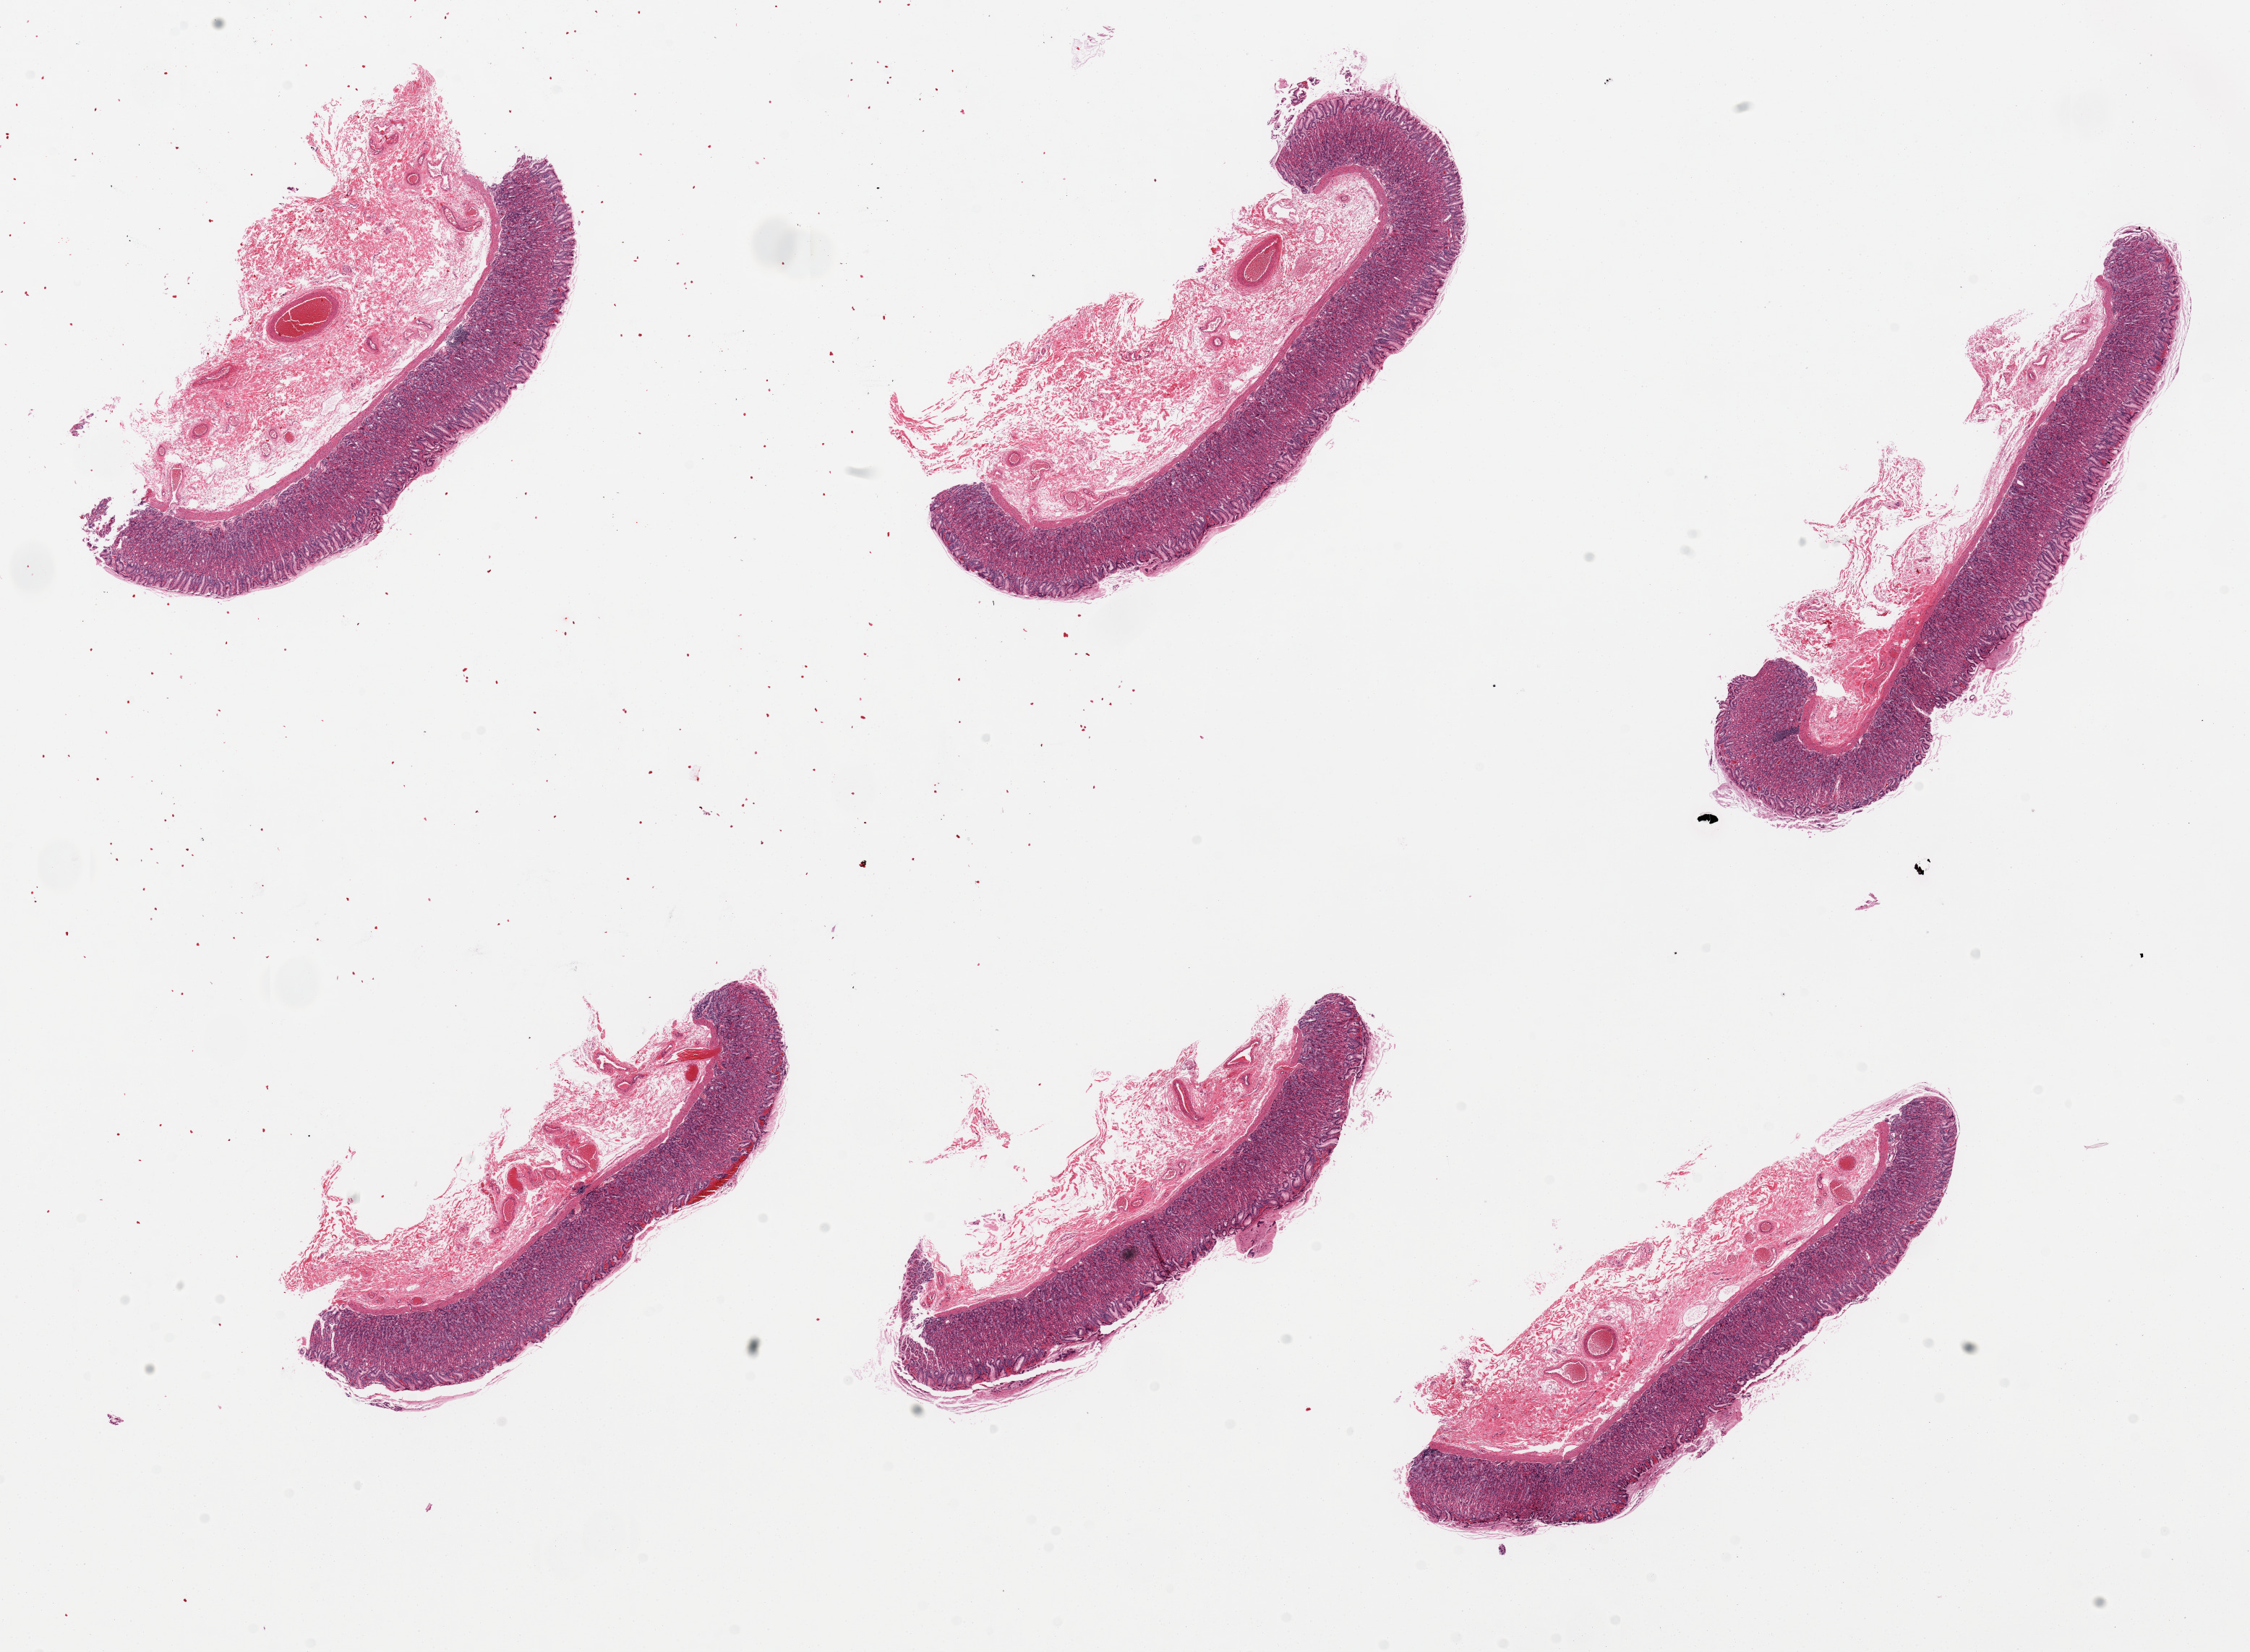
Haematoxylin and eosin whole-slide image, whole scanned area (about 24.6 x 18.1 mm, from a 20x scan) shown as a low-resolution overview, PAXgene-fixed paraffin-embedded (PFPE) section, target tissue: stomach, tissue donor sample. Female donor.
Pathologist's review note for this sample: 6 pieces, mucosa and submucosa.